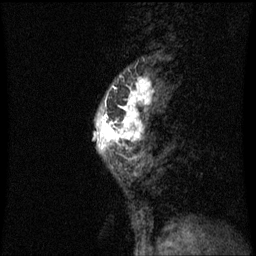
Breast MRI (dynamic contrast-enhanced), one sagittal slice. Slice 22 of 60 in the series (ordered by position). Dynamic contrast-enhanced series, image 2 of 3 at this slice position (ordered by acquisition). 1.5 T. TE 4.2 ms, TR 8.9 ms. 256 × 256 image matrix, field of view 200 × 200 mm. Patient: female, 50 years. From the clinical record (not read from this slice): setting: breast cancer imaged before/during neoadjuvant chemotherapy; receptor status: triple-negative.
Structures marked on this image (semi-automatic segmentation, software-assisted and operator-edited):
- analysis volume of interest (the breast-tissue region the enhancement analysis was run in; not a lesion): bounding box [x1, y1, x2, y2] px = [94, 80, 161, 171]
- tumour enhancement mask (voxels above the 70 % enhancement threshold inside the analysis volume of interest): [102, 80, 151, 149]